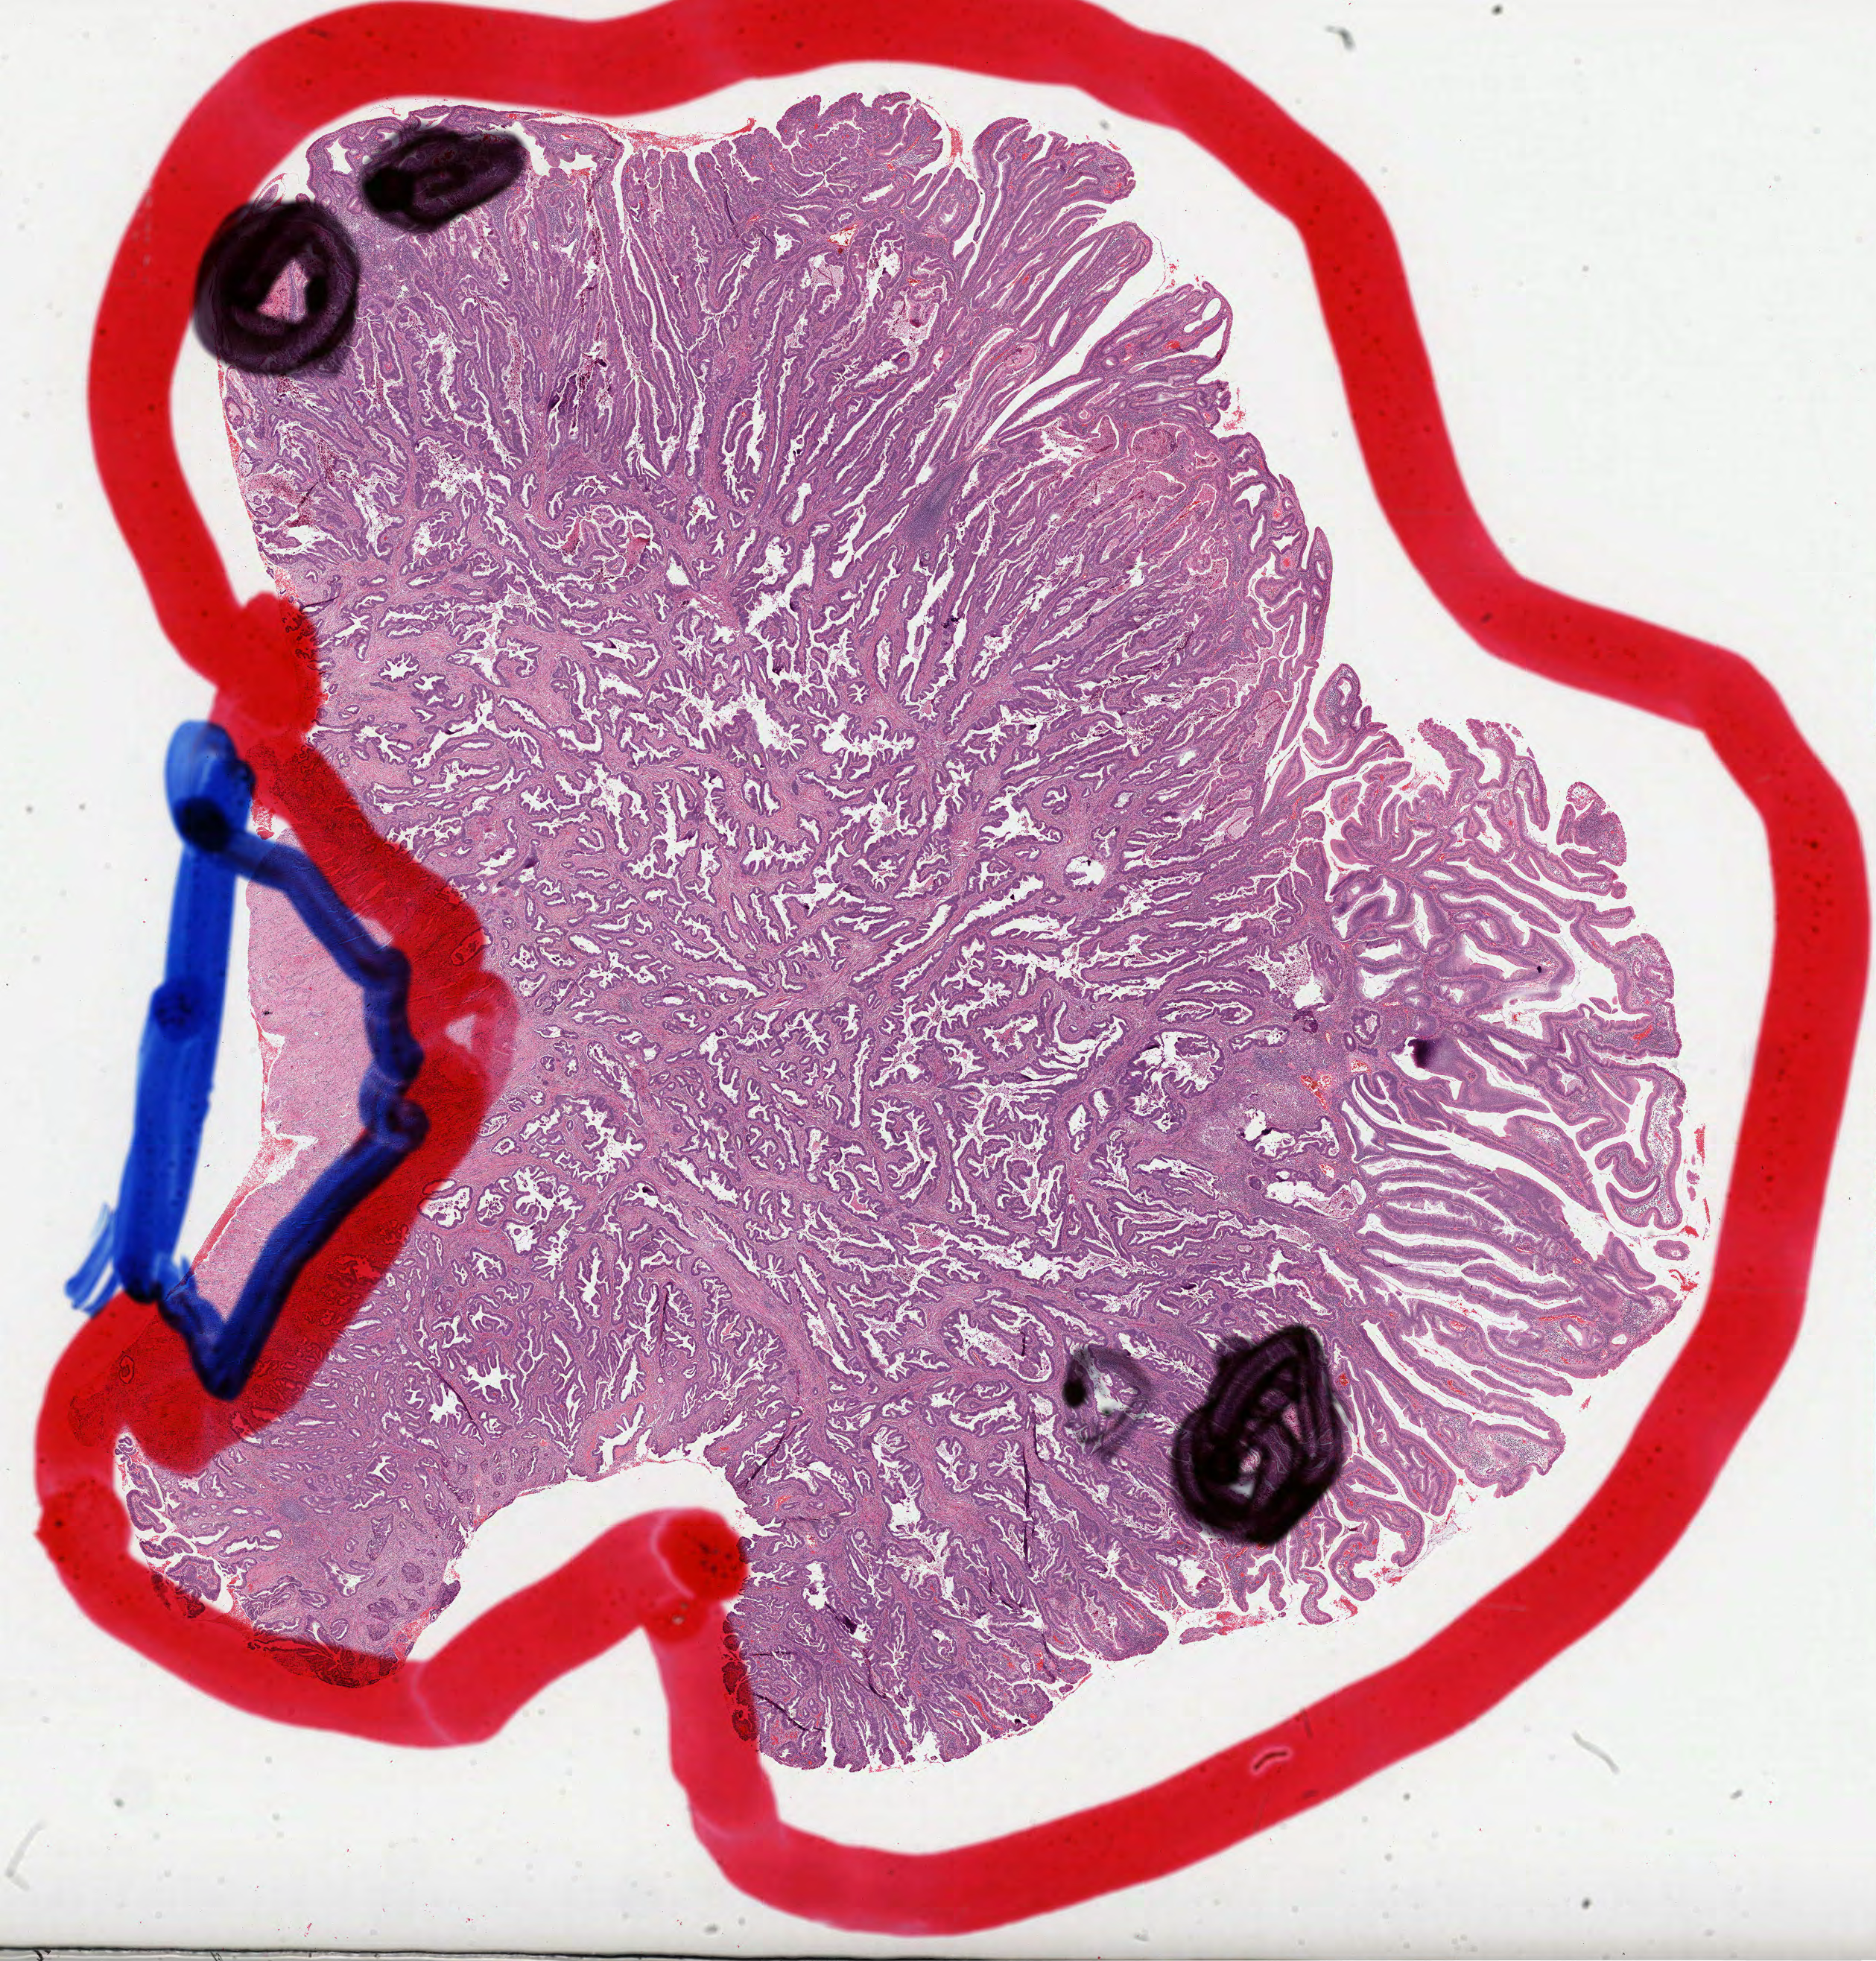
Digitized Hematoxylin and eosin (H&E) stained tissue section (whole slide), whole scanned area (about 20.3 x 21.2 mm, from a 40x scan) shown as a low-resolution overview; formalin-fixed paraffin-embedded (FFPE) diagnostic section; sample: primary tumour, colon. Female, age 59 years at initial diagnosis.
* histologic diagnosis: Adenocarcinoma, NOS (sigmoid colon)
* TNM: T2 N0 M0
* AJCC pathologic stage: I (7th edition)